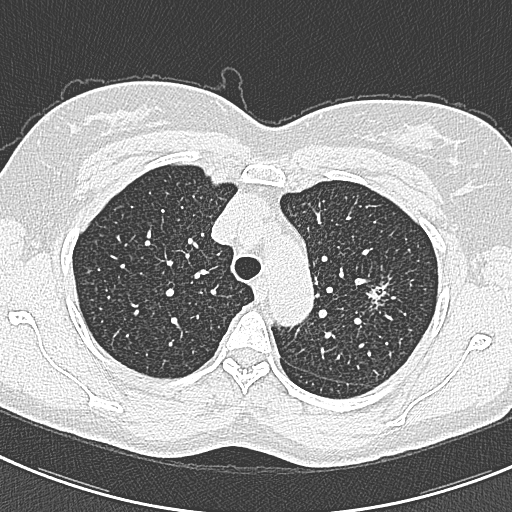
Chest CT (low-dose screening protocol), one axial image, first (baseline) screen, lung window (W 1500 / L -600 HU), lung (sharp) reconstruction kernel (B80f), slice 68 of 309 in the series, 512 × 512 image matrix. Female participant, aged 57 years at enrolment.
• Expert reader's lesion annotation, box from (x=362, y=270) to (x=412, y=323) px.
• The screening reader recorded 2 non-calcified nodules or masses ≥4 mm on this exam (right lower lobe, left upper lobe); which of them this box marks is not recorded.
• Official screen result: positive, change unspecified: nodule(s) >= 4 mm or enlarging nodule(s), mass(es), or other non-specific abnormalities suspicious for lung cancer.
• Later outcome: lung cancer diagnosed 198 days after this screen — adenocarcinoma, NOS, left upper lobe, well differentiated (G1), stage IA (AJCC 6th edition), 10 mm at pathology.